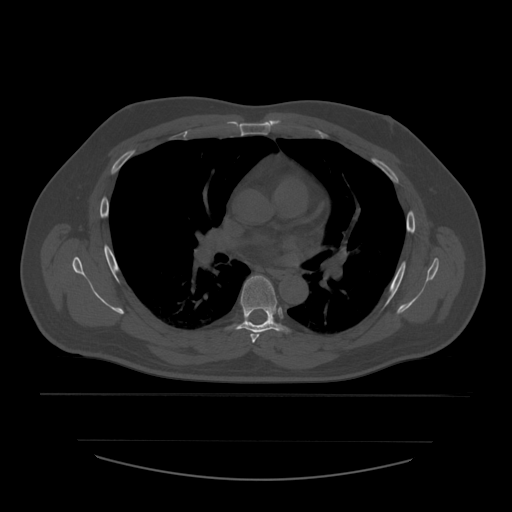
CT including the spine, one axial slice. Position 381 of 532 along the scan axis. 120 kVp. Bone window (W 1800 / L 400 HU). 1.25 mm slice thickness. 512 × 512 image matrix, field of view 441 × 441 mm. Patient age 44 years. From the clinical record (not read from this slice): primary cancer: soft tissue sarcoma.
Annotated regions visible in this slice (semi-automatic segmentation, software-assisted and operator-edited):
- T5 vertebra: bounding box <250,332,260,343> (left, top, right, bottom; pixels)
- T6 vertebra: <236,276,289,333>